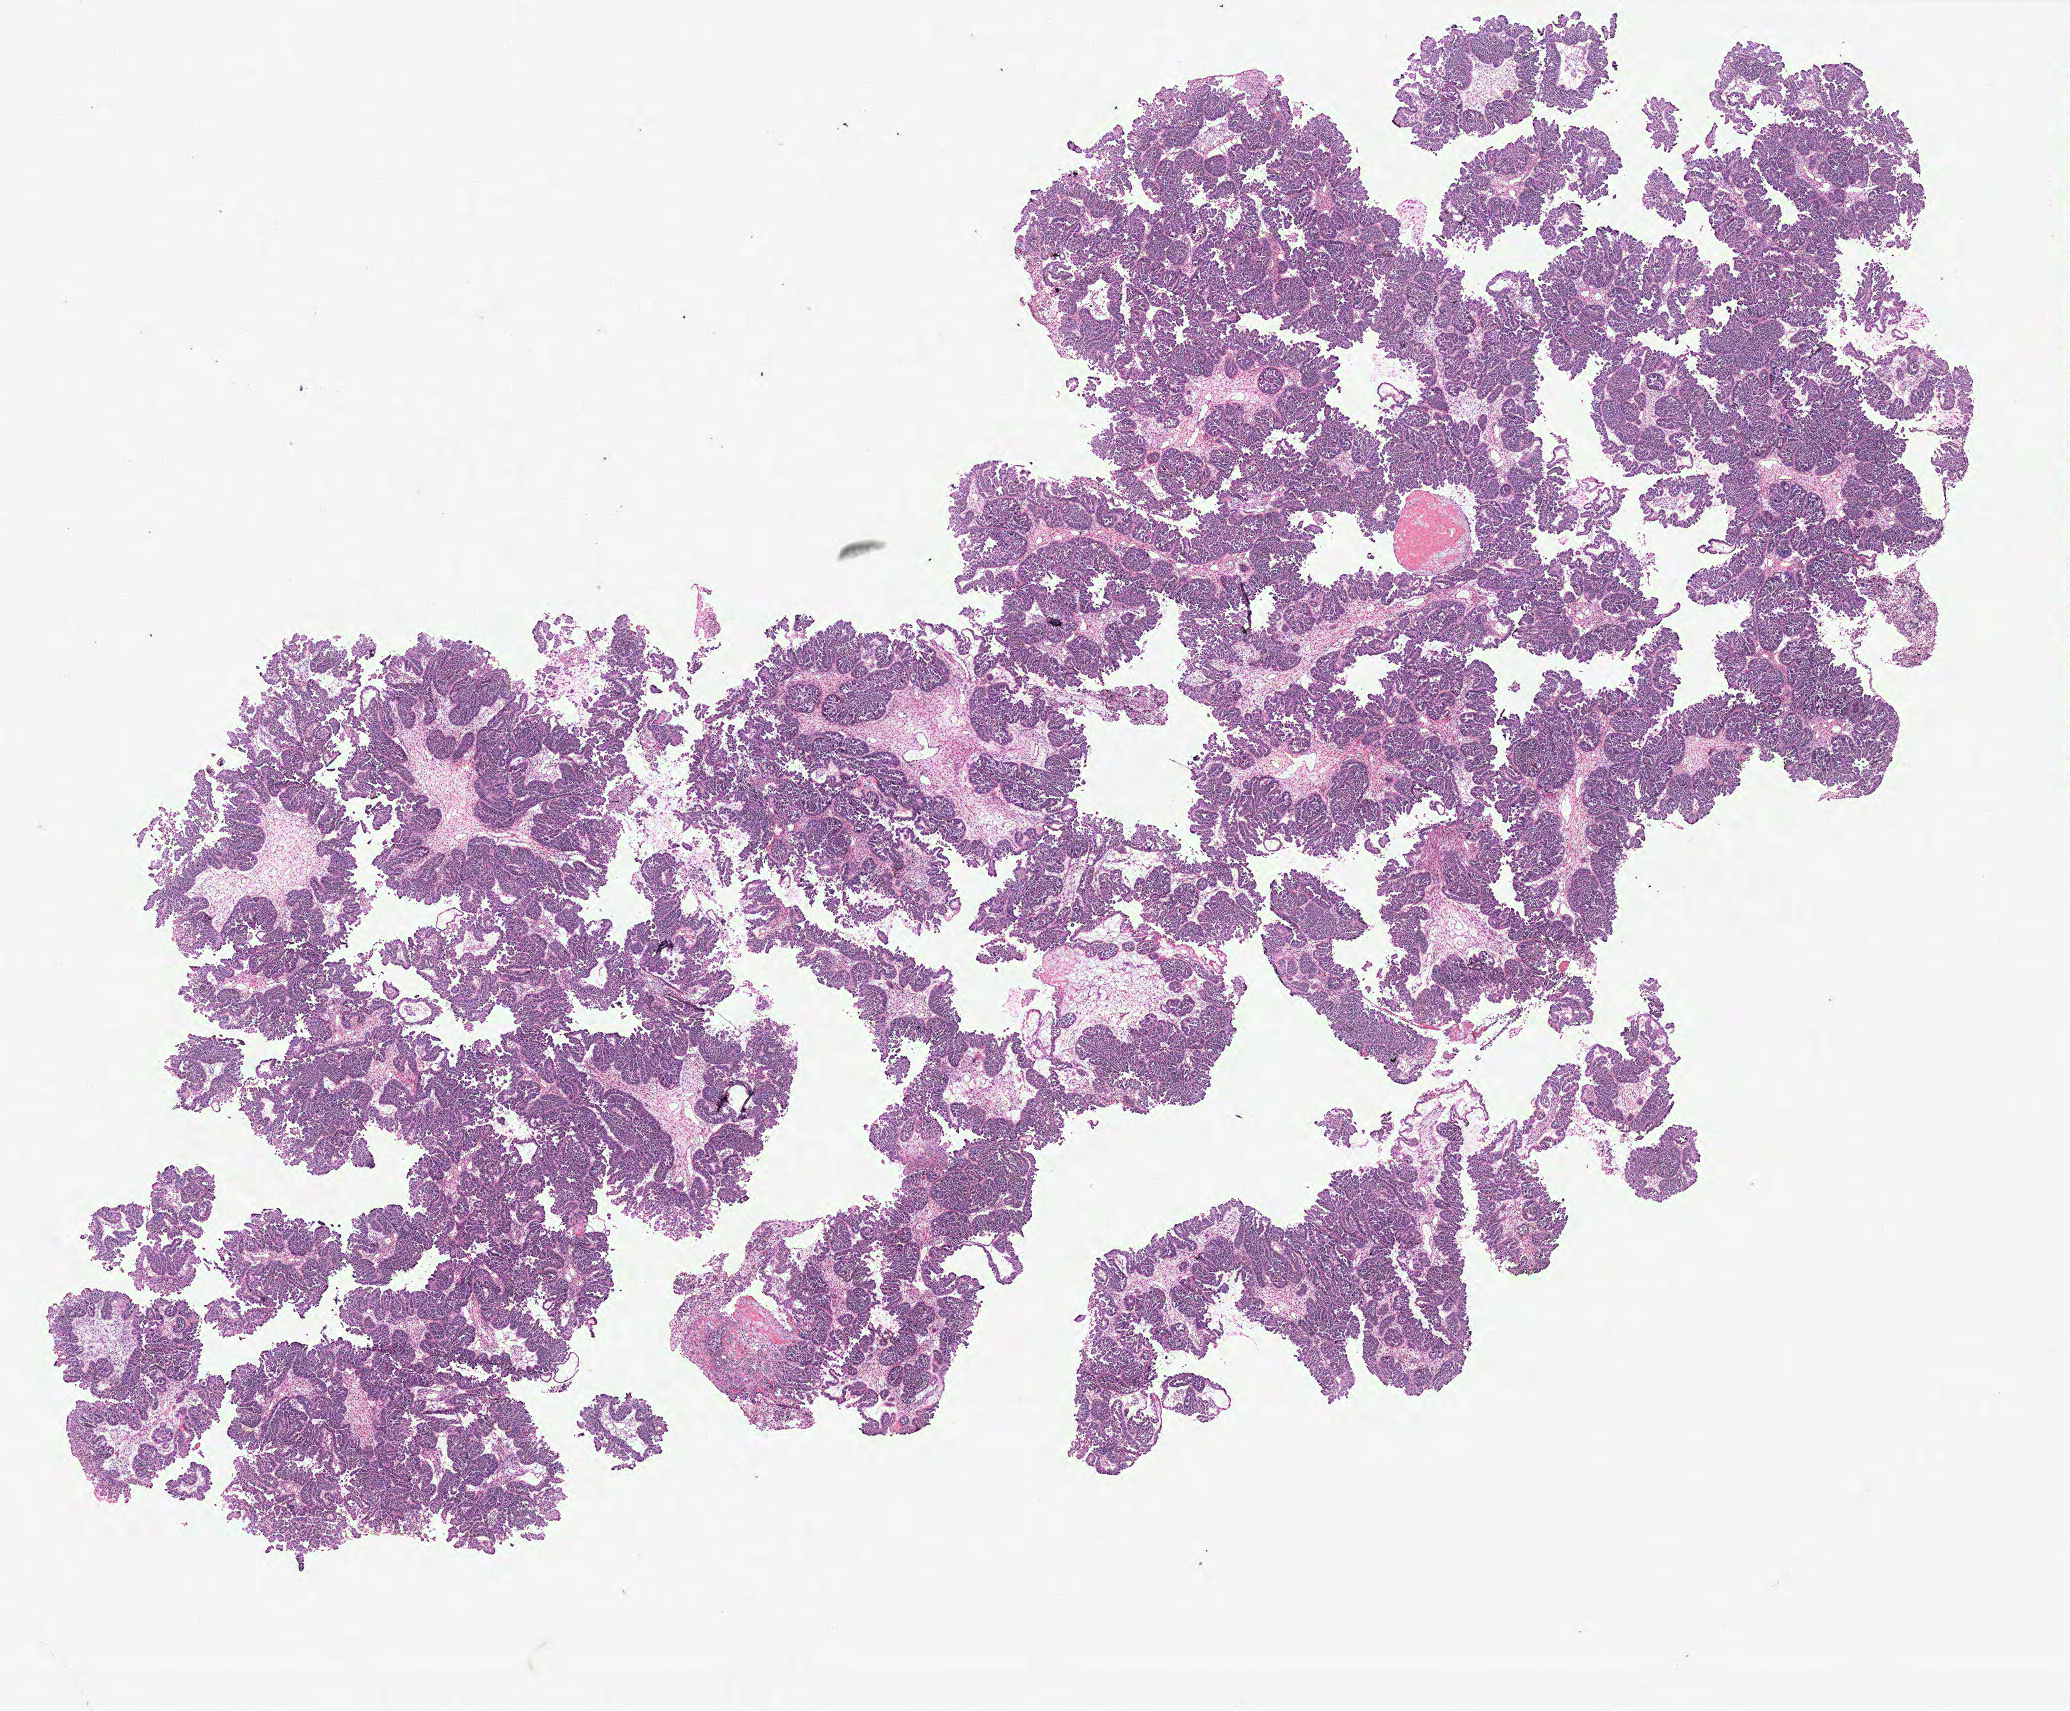
Hematoxylin and eosin (H&E) stained whole-slide image — low-resolution overview of the scanned area, about 16.6 x 13.7 mm; ovary, tumour tissue. Patient: female, age 48 years.
Primary tumour site (as recorded): fallopian tube. Diagnosis: Serous adenocarcinoma, NOS (fallopian tube).